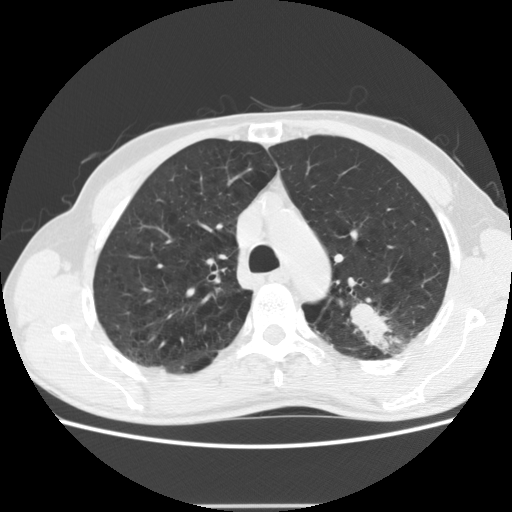
Chest CT (low-dose screening protocol), one axial image. Baseline screening round. Lung window (W 1500 / L -600 HU). Slice 49 of 191 in the series. 512 × 512 image matrix. Male, age 64 years at enrolment.
- Expert-annotated lung lesion, bounding box <339,282,438,360> (left, top, right, bottom; pixels).
- Screening reader's record for this exam (one nodule recorded; not confirmed to be the boxed lesion): non-calcified nodule or mass ≥4 mm, left upper lobe, 27 × 19 mm, poorly defined margins, soft tissue attenuation.
- Participant outcome: lung cancer diagnosed 23 days after this screen — adenocarcinoma, NOS, left upper lobe, moderately differentiated (G2), stage IA (AJCC 6th edition), 29 mm at pathology.